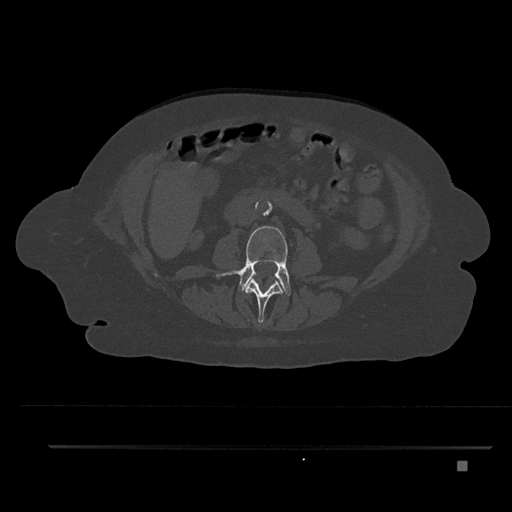
CT including the spine, one axial slice. Slice 146 of 797 in the series (ordered by position). 120 kVp. Bone window (W 1800 / L 400 HU). 512 × 512 image matrix, field of view 437 × 437 mm. Patient: female, 76 years. From the clinical record (not read from this slice): primary cancer: lung.
Structures marked on this image (semi-automatically segmented with operator editing):
- L2 vertebra: bounding box (x1, y1, x2, y2) in pixels: (245, 279, 283, 324)
- L3 vertebra: (216, 226, 291, 296)